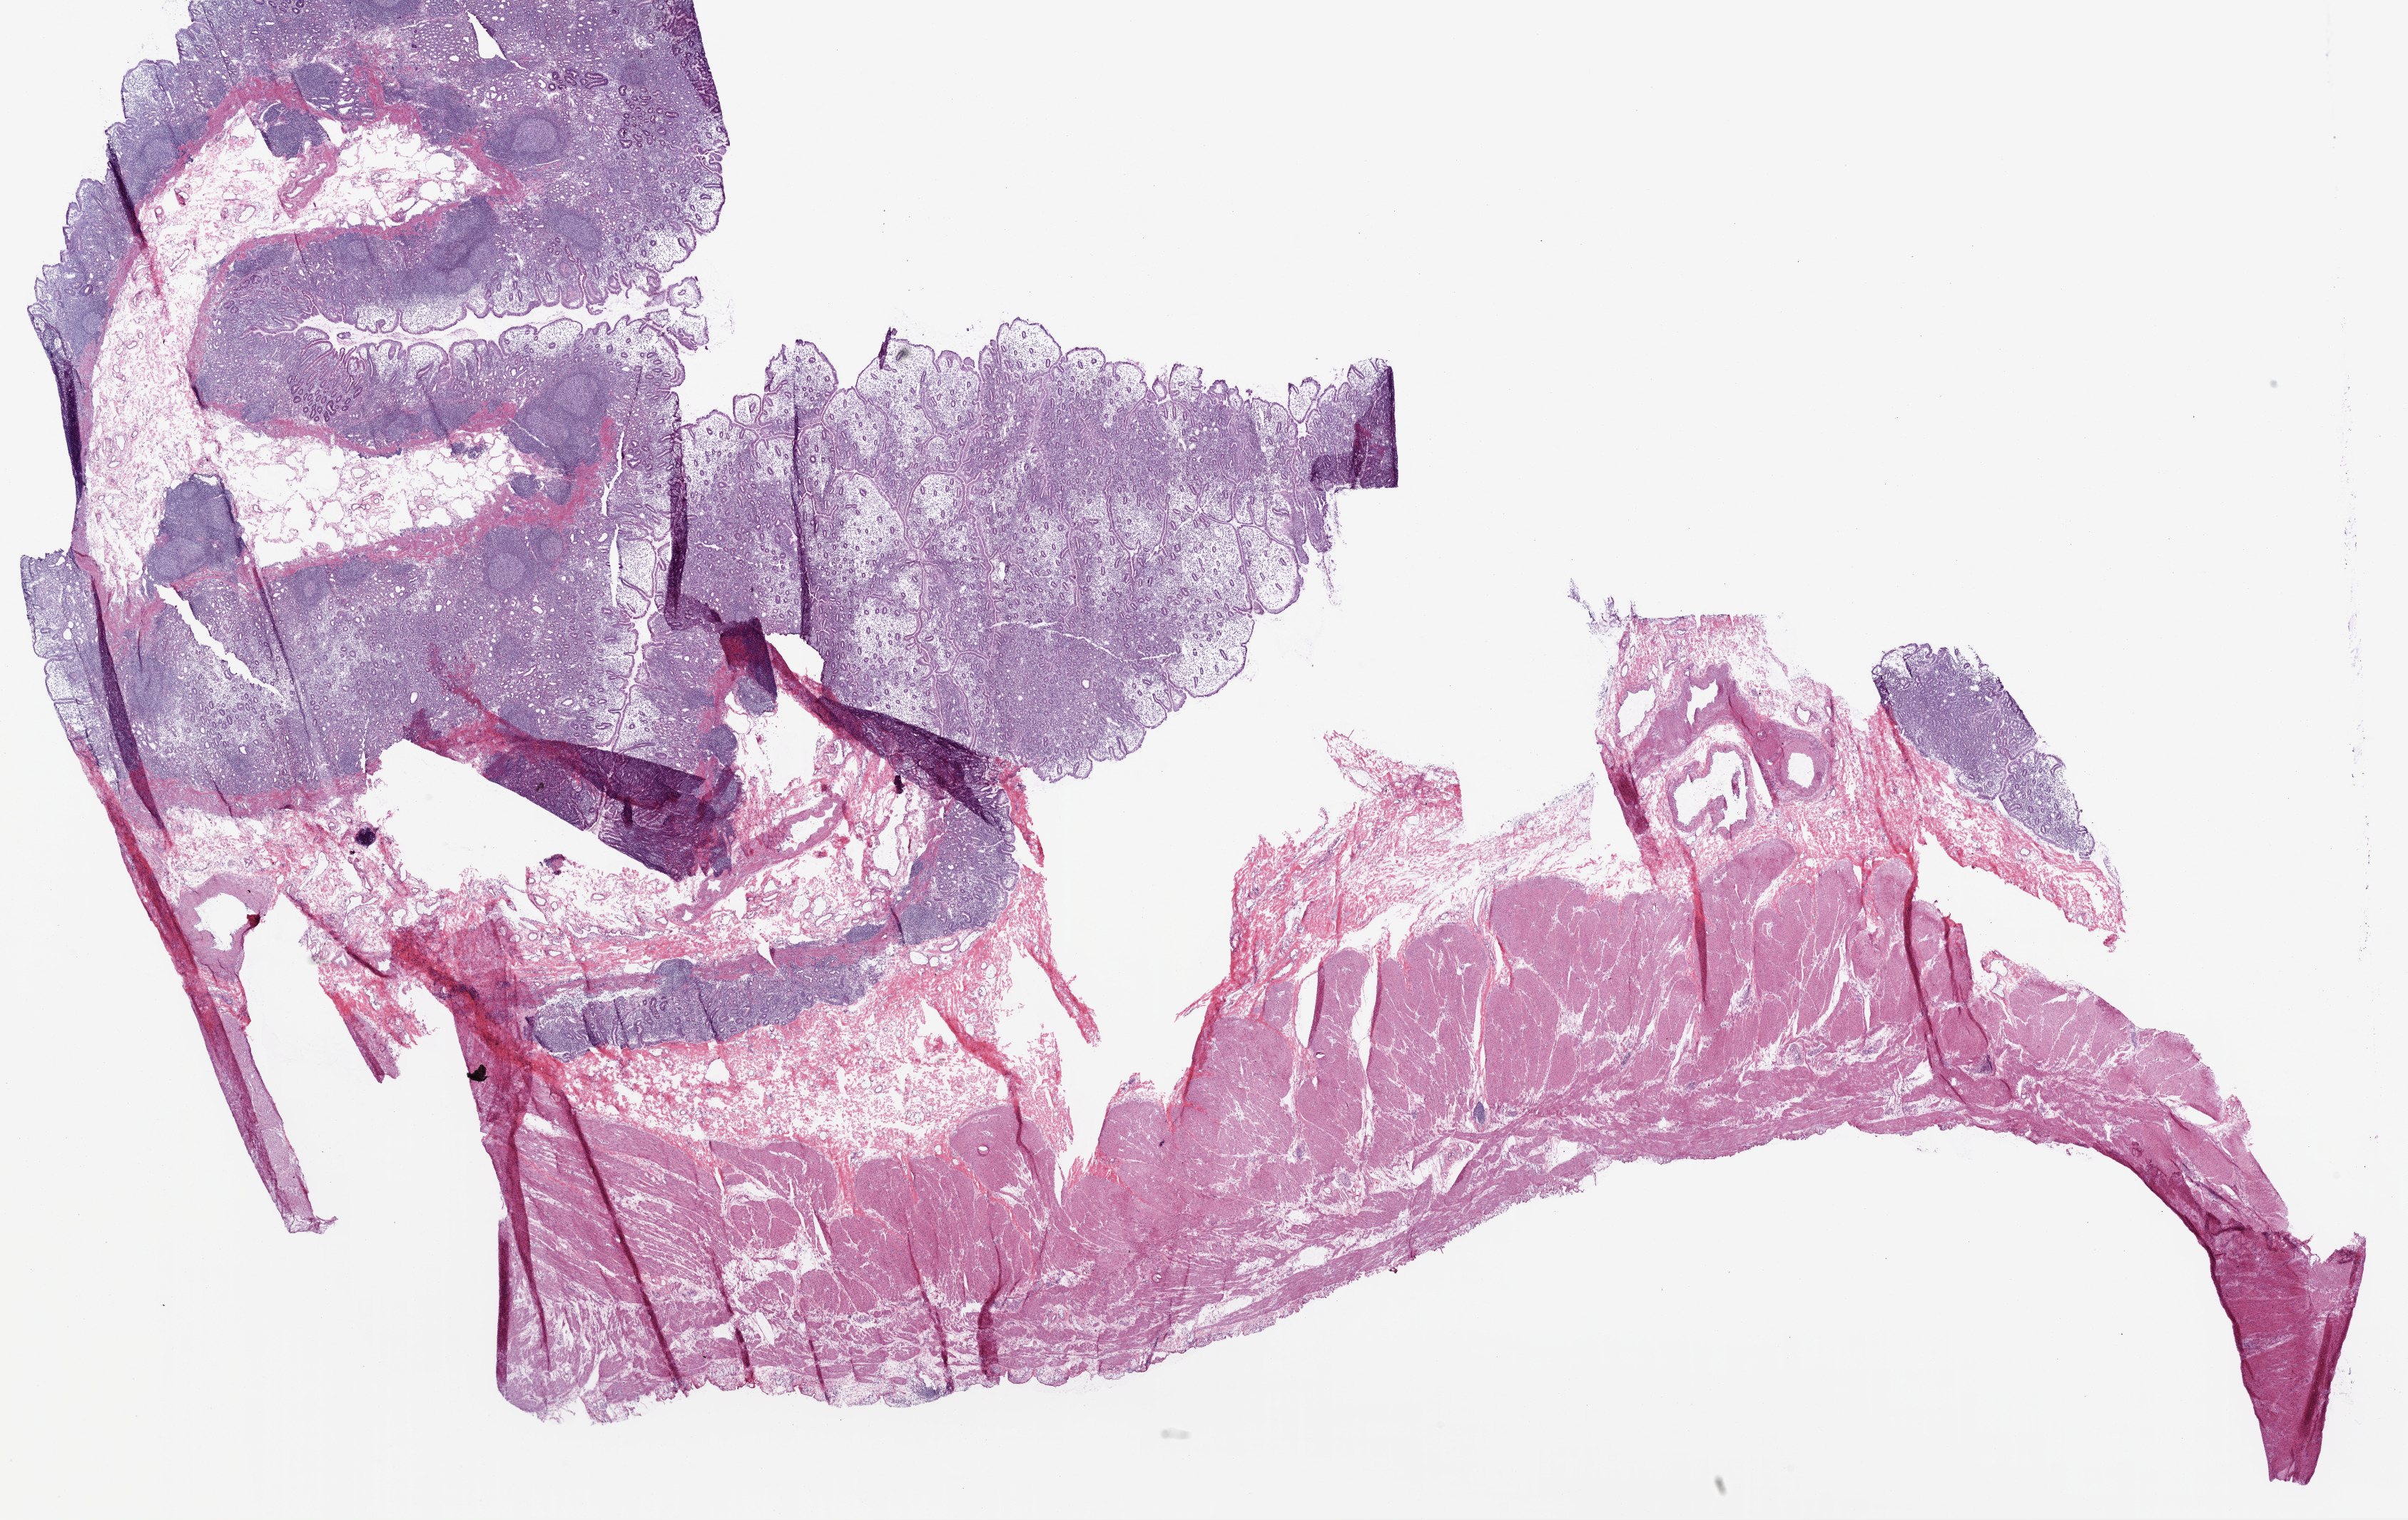
Whole-slide histology image, Hematoxylin and eosin (H&E) stained, shown as a low-resolution overview of the whole scanned area (about 27.1 x 17.1 mm, from a 20x scan); frozen section from the top of the tissue portion; solid tissue normal (non-tumour tissue) sample from the stomach. Female patient; age at initial diagnosis 74 years.
This section: solid tissue normal (non-tumour) sample from the same patient. Patient diagnosis: Adenocarcinoma, NOS.